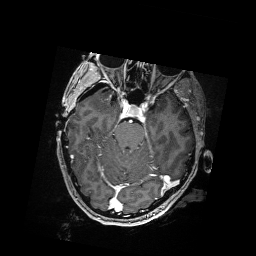
Brain MRI from a brain-tumour surgery series, one axial slice. Position 116 of 176 along the scan axis. T1-weighted post-contrast. 1 mm slice thickness. 256 × 256 image matrix, field of view 256 × 256 mm. Case-level facts recorded for this patient, not image findings: histopathology: Metastatic Carcinoma from Breast primary; tumour location: Right Frontal.
Outlined on this slice (expert manual segmentation):
- residual tumour: box from (x=92, y=88) to (x=95, y=91) px